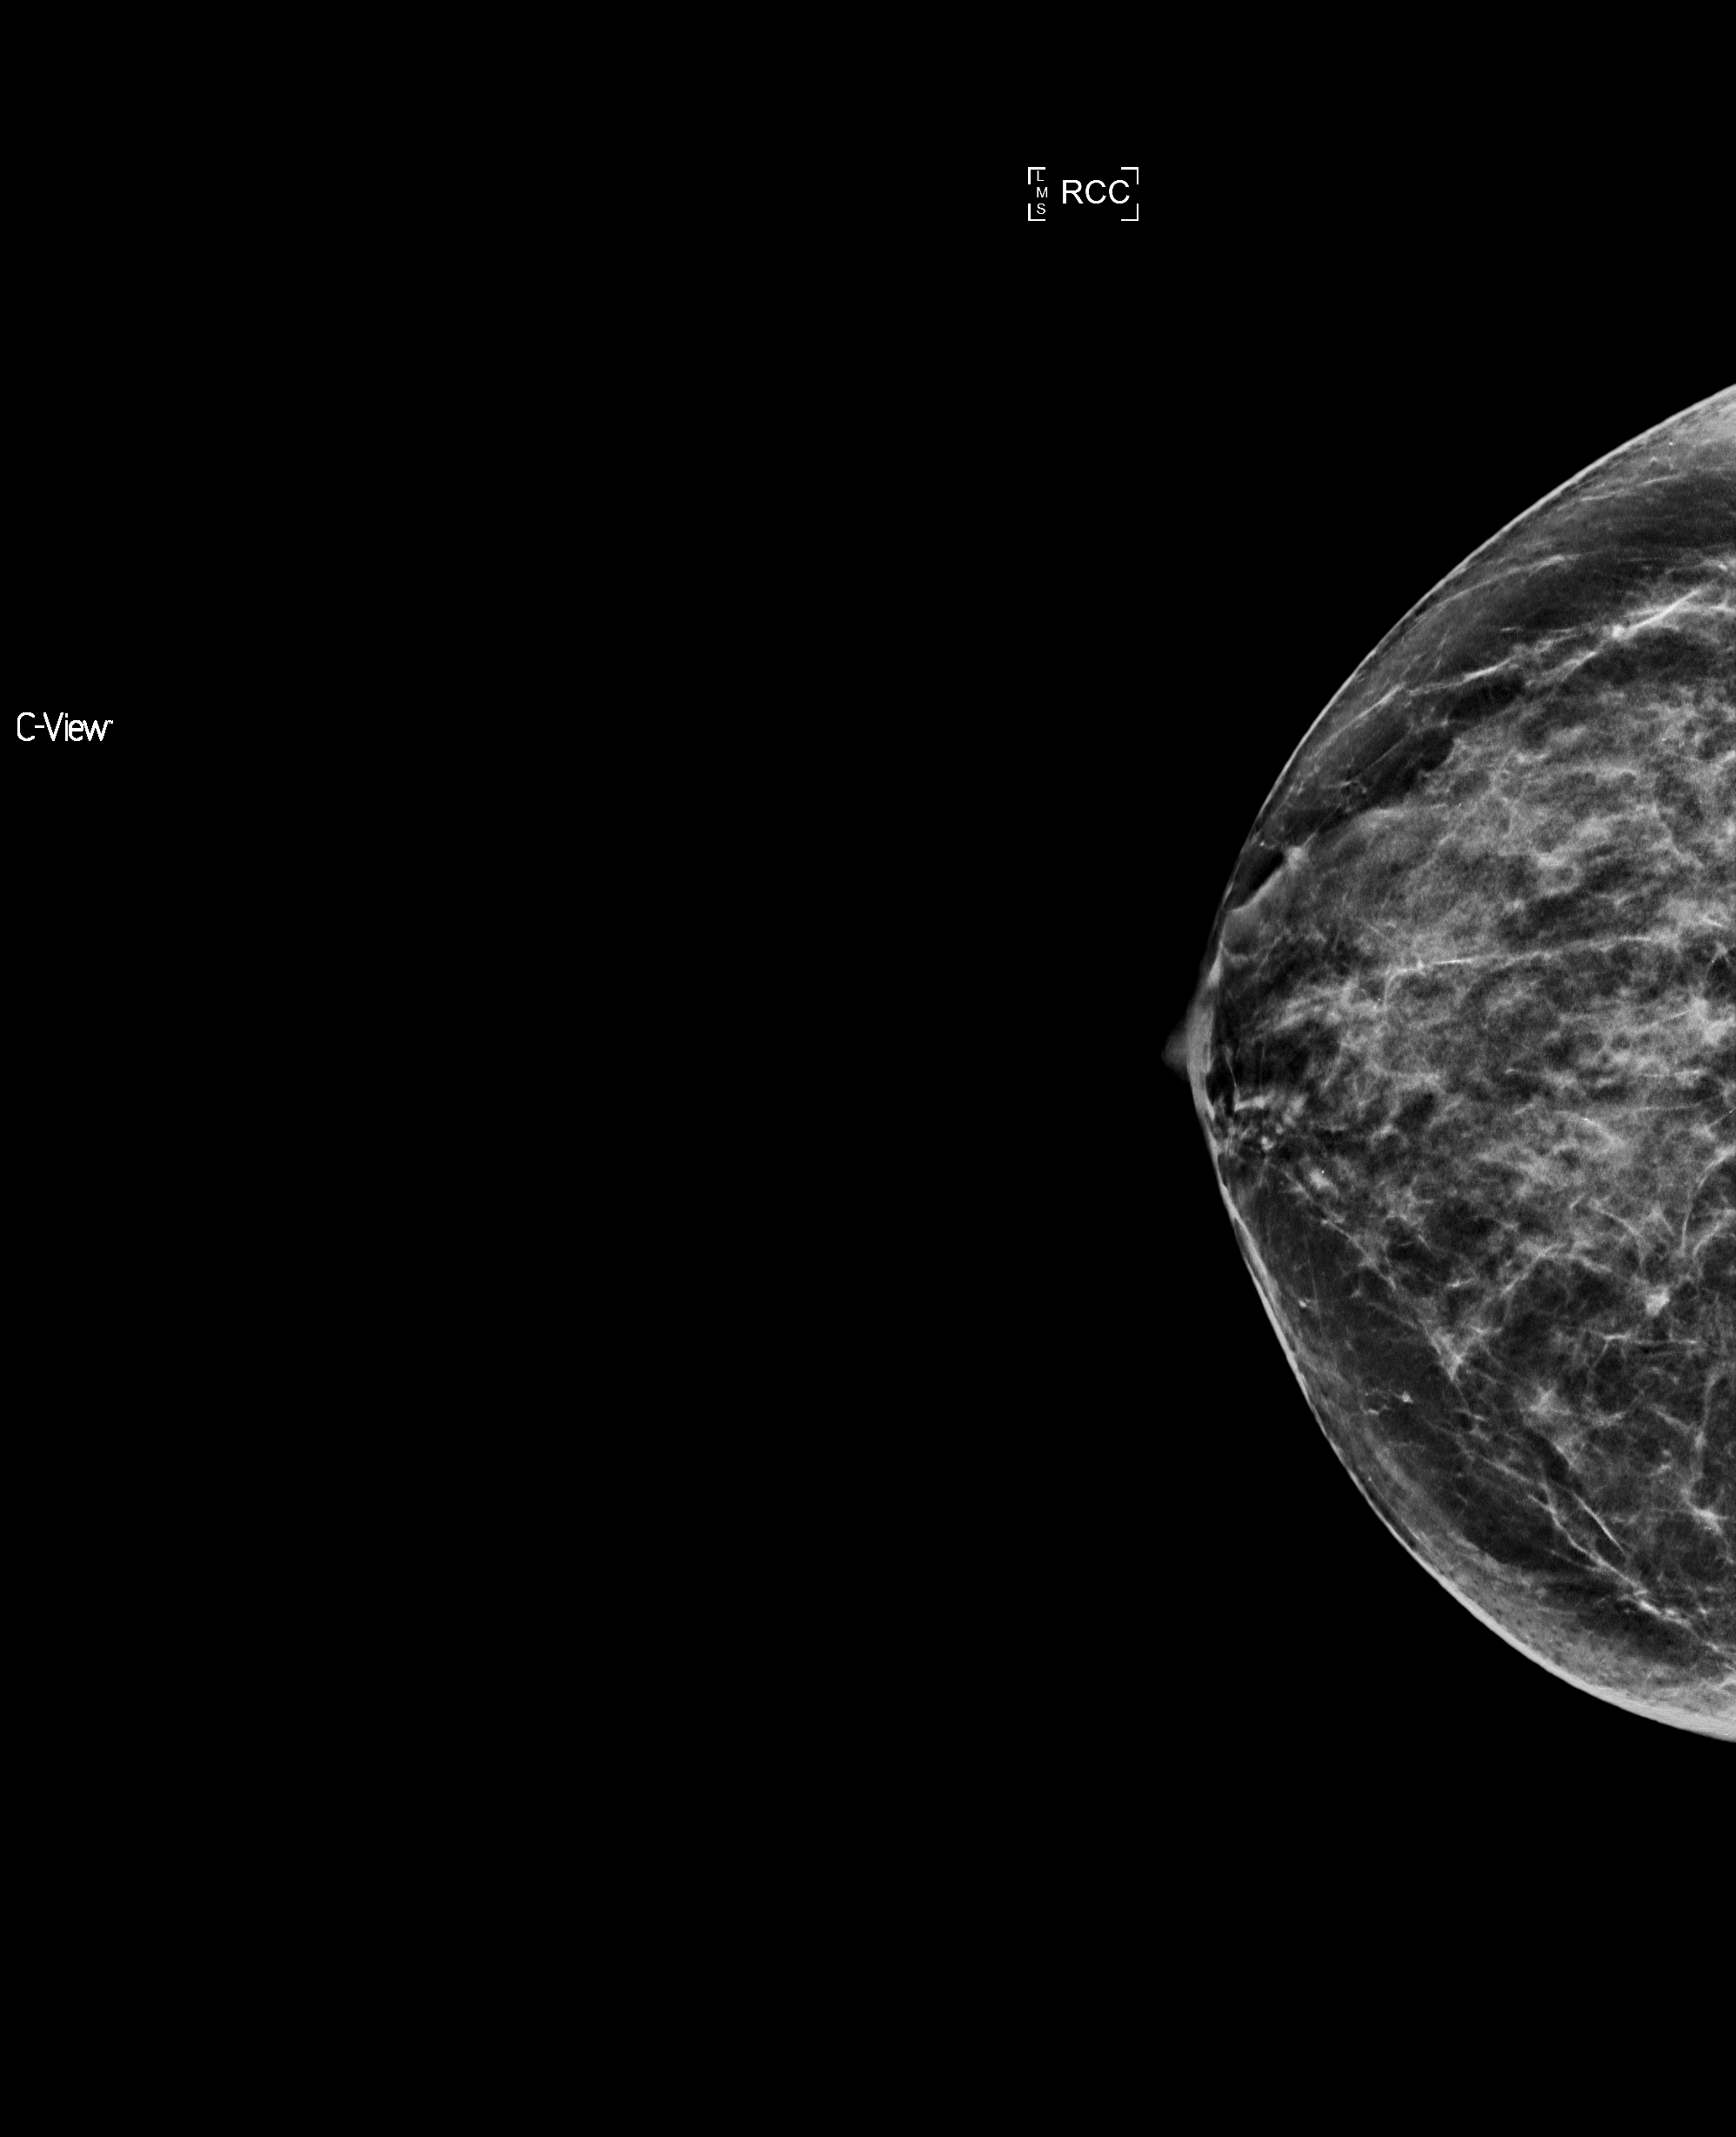
Full-field digital mammogram (FFDM), right breast, CC view, annual screening mammography examination. Patient aged 59 years (female).
BI-RADS breast density category at the screening exam (both breasts, scale 1–4): 3. Final BI-RADS category for the screening round (tomosynthesis exam, both breasts): category 1. Recall: no recall after this screen.